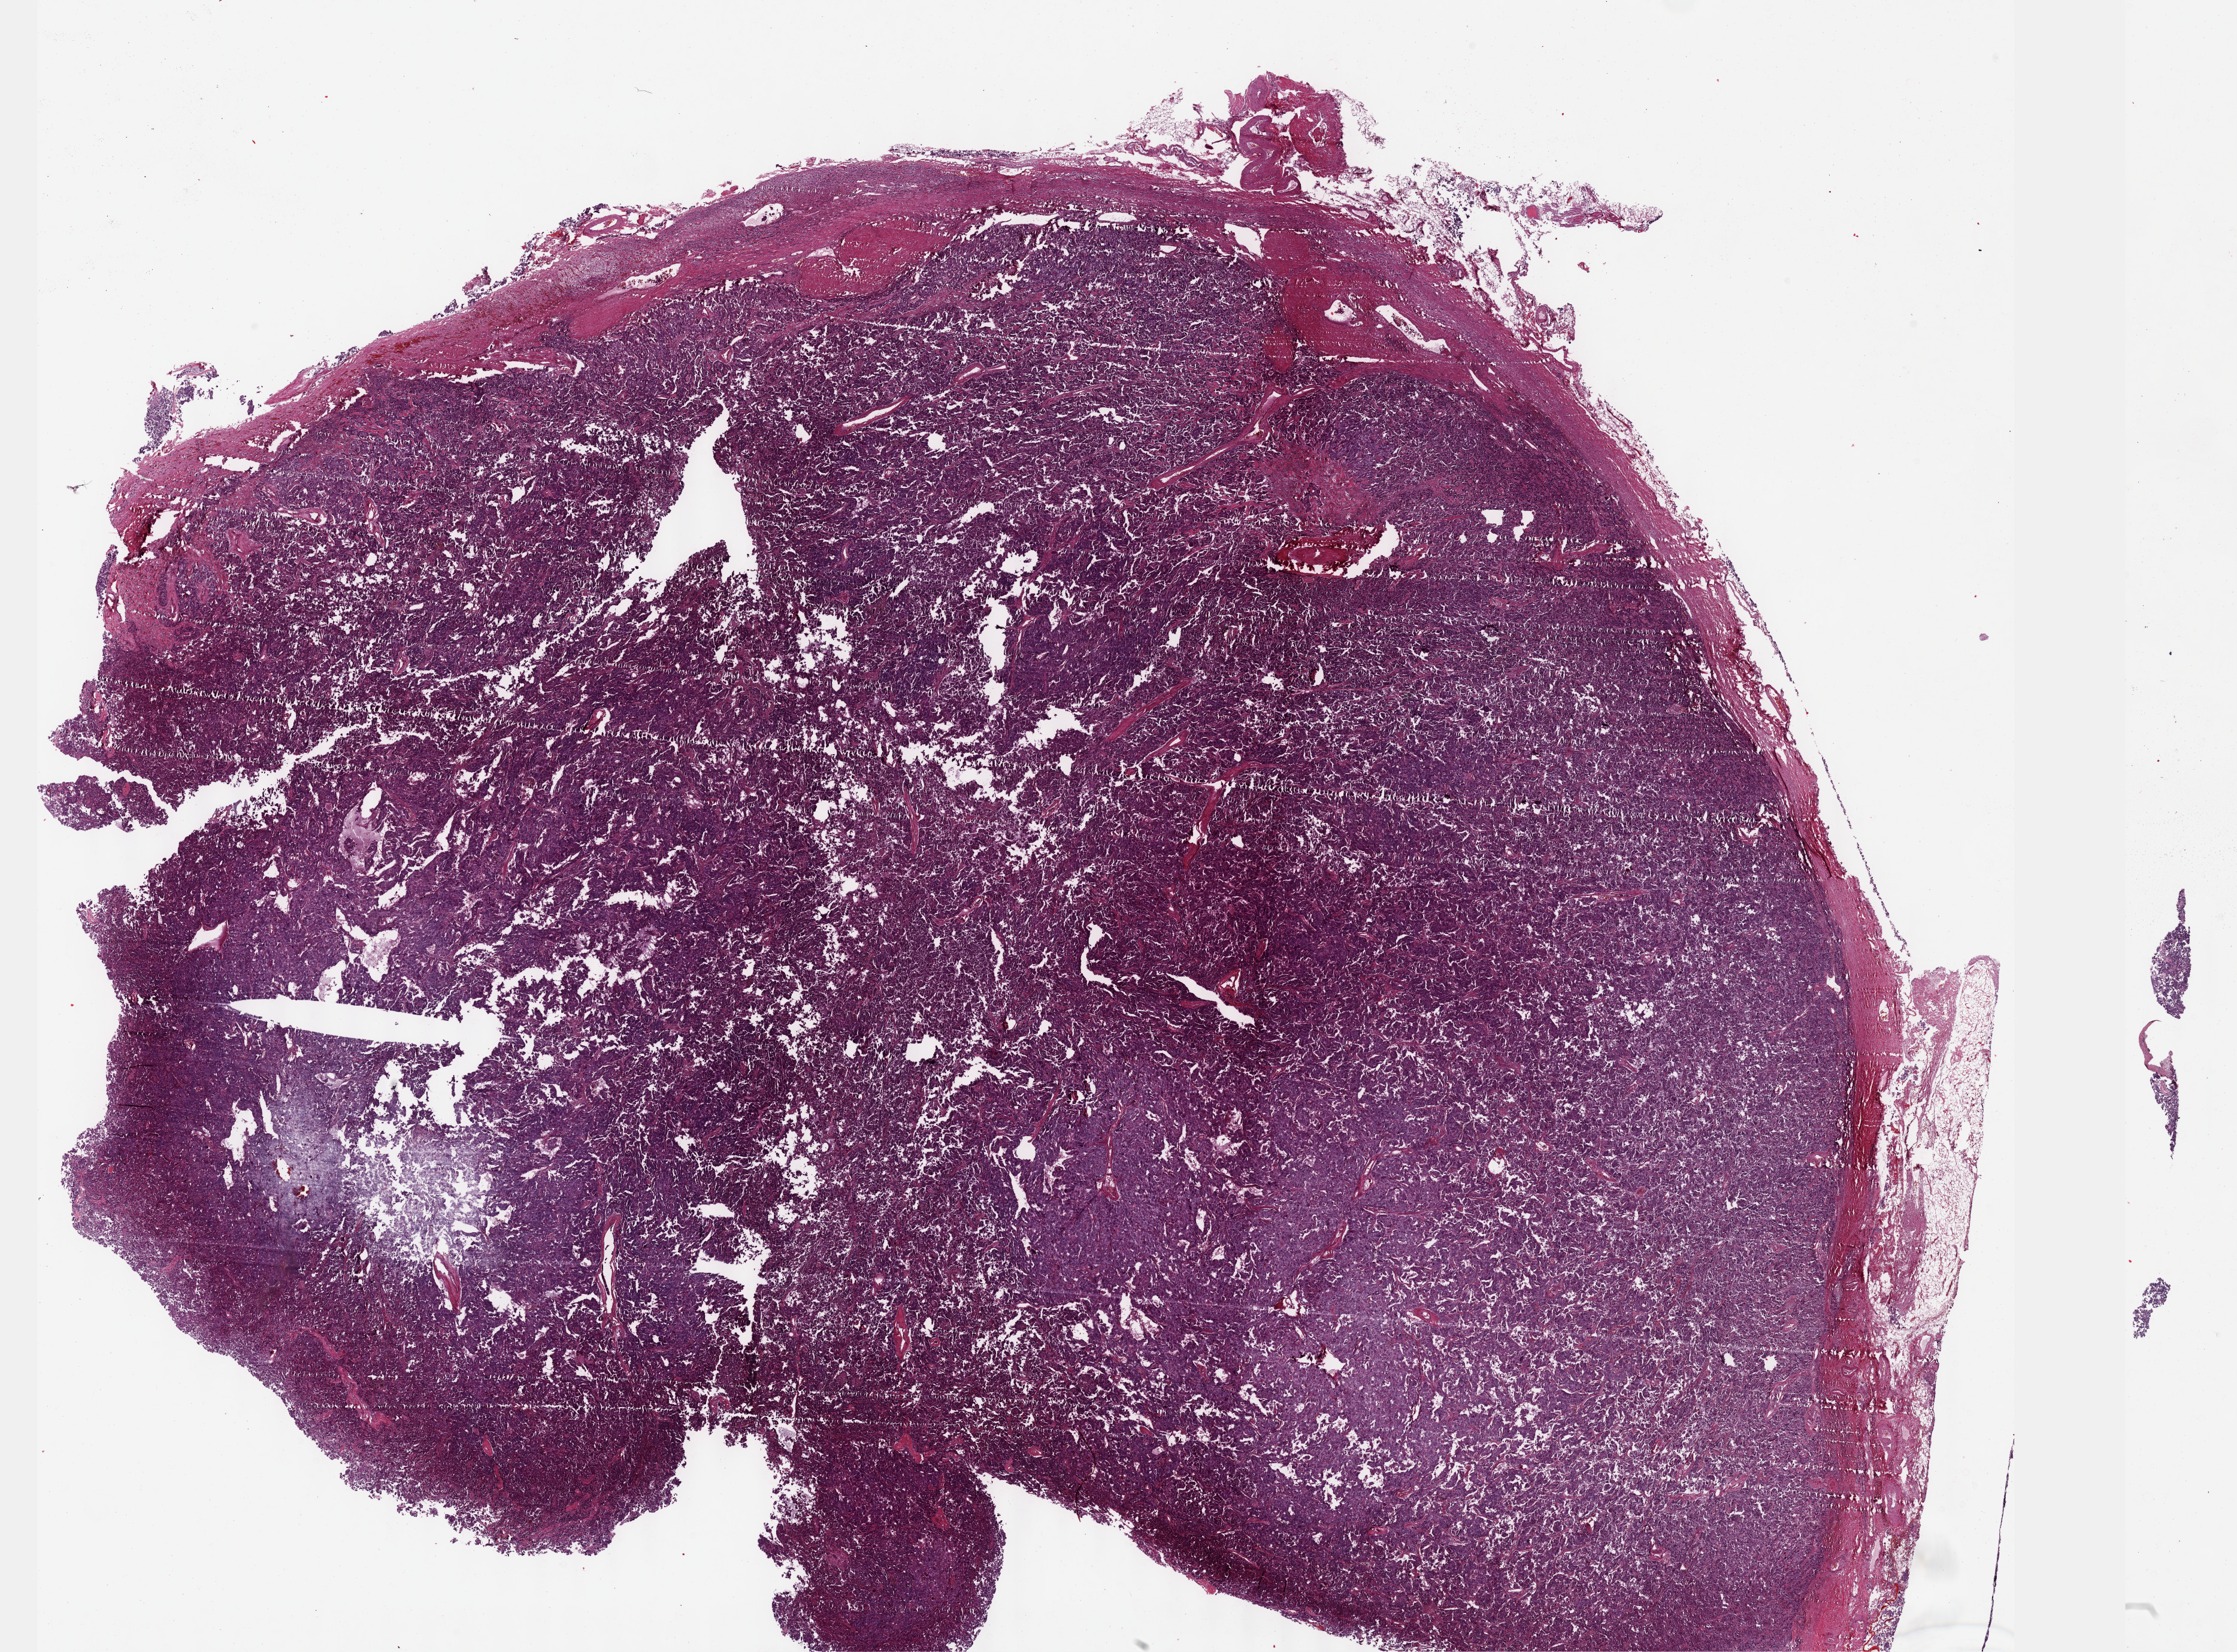
Whole-slide histology image, H&E-stained, a low-resolution overview of the entire scanned area, about 30.2 x 22.3 mm (slide scanned at 40x), formalin-fixed paraffin-embedded (FFPE) diagnostic section, primary tumour sample from the adrenal gland. Patient: female, age at initial diagnosis 44 years.
* pathologic diagnosis: Pheochromocytoma, NOS